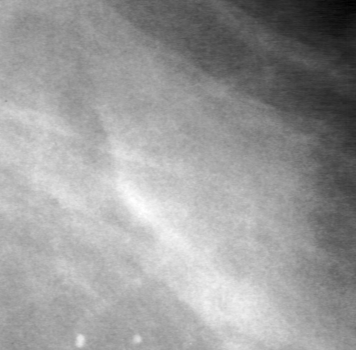
Cropped region of a digitized screen-film mammogram centred on a radiologist-marked abnormality; left breast; CC view; BI-RADS breast density category 1 (scale 1–4).
Finding: mass, shape irregular, margins obscured; BI-RADS assessment category 0 (incomplete: needs additional imaging); pathology result (as recorded, not read from the image): benign.